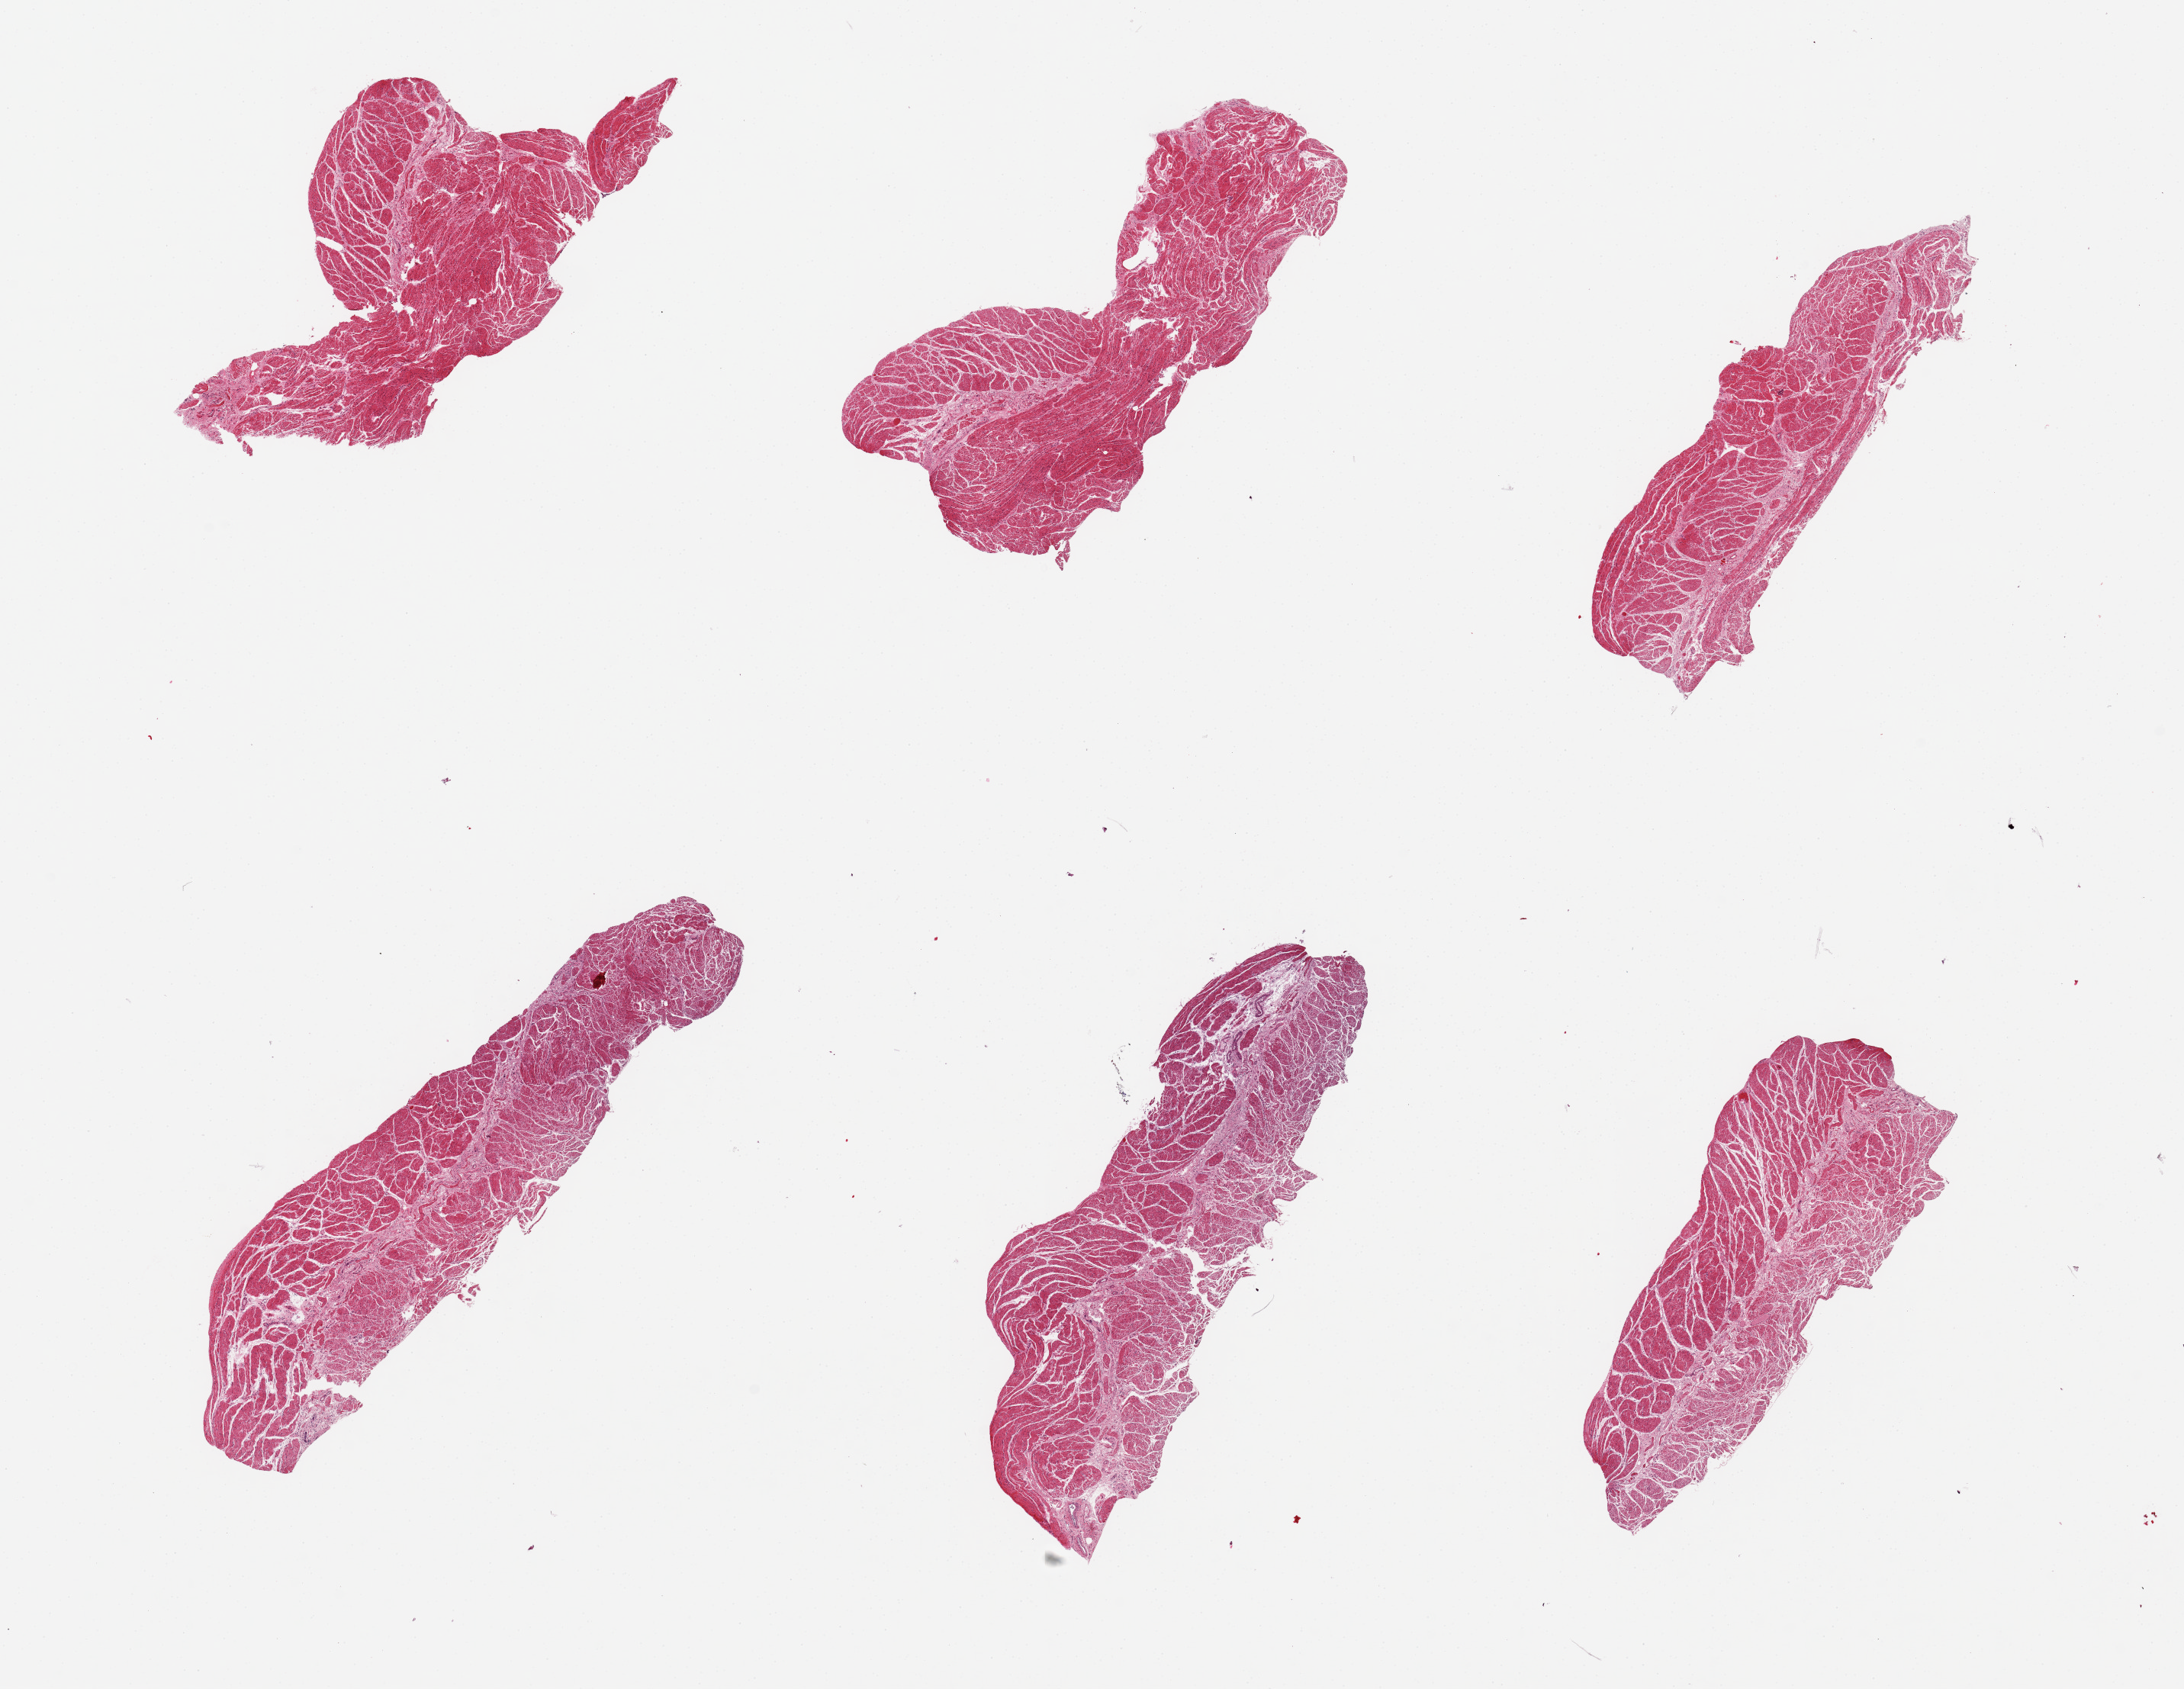
Digitized H&E-stained section, brightfield — whole scanned area (about 22.6 x 17.5 mm, slide scanned at 20x) shown as a low-resolution overview, PAXgene-fixed paraffin-embedded (PFPE) section, target tissue: esophageal muscle, donor tissue sample. Male donor.
Pathologist's review note for this sample: 6 pieces, all muscularis.